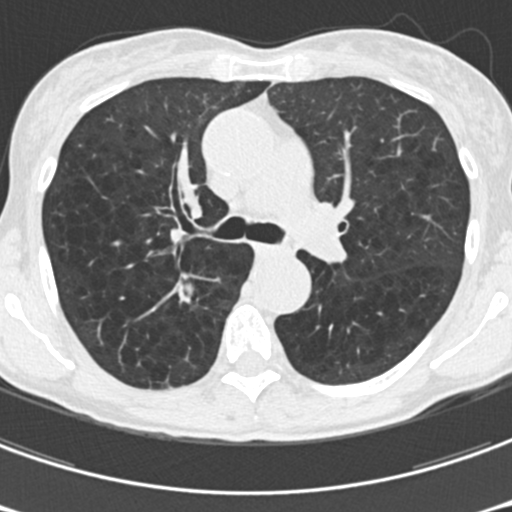
Low-dose screening chest CT, one axial slice. Position 111 of 176 along the scan axis. 120 kVp. Lung window (W 1500 / L -600 HU). 2 mm slice thickness. 512 × 512 image matrix, field of view 277 × 277 mm.
Structures marked on this image (expert manual segmentation):
- lesion 1 (tumor, upper lobe of right lung): bounding box <177,285,192,303> (left, top, right, bottom; pixels)